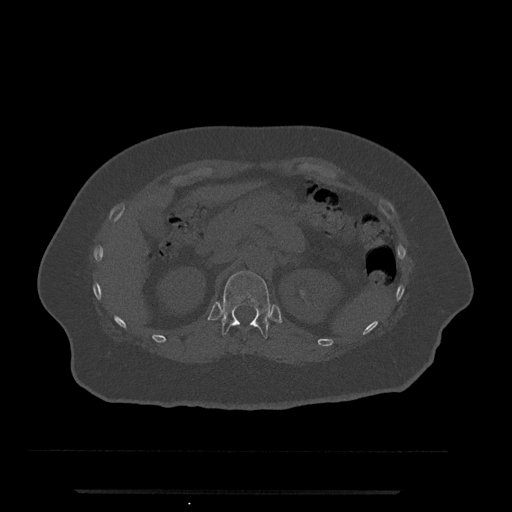
CT including the spine, one axial slice; slice 175 of 797 in the series (ordered by position); reconstruction kernel Br40s/3; 120 kVp; bone window (W 1800 / L 400 HU); 0.5 mm slice thickness; 512 × 512 image matrix, field of view 440 × 440 mm. Female patient, age 51 years. Case-level facts recorded for this patient, not image findings: primary cancer: neuro; vertebrae with lytic lesions (as recorded): T8.
Annotated regions visible in this slice (semi-automatically segmented with operator editing):
- T12 vertebra: bounding box <221,271,271,339> (left, top, right, bottom; pixels)